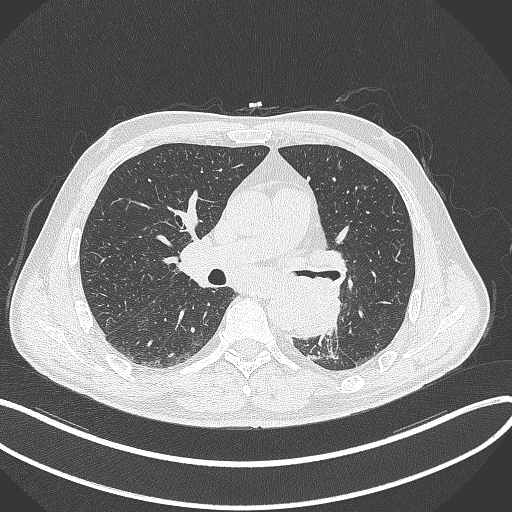
Chest CT, one axial slice; slice 189 of 329 in the series (ordered by position); 120 kVp; lung window (W 1500 / L -600 HU); 1 mm slice thickness; 512 × 512 image matrix. Patient: male, 59 years. From the clinical record (not read from this slice): clinical TNM (as recorded): T2a N2 M0.
Outlined on this slice (bounding box drawn by a radiologist):
- lung tumour (recorded histology: squamous cell carcinoma): bounding box <294,275,340,342> (left, top, right, bottom; pixels)